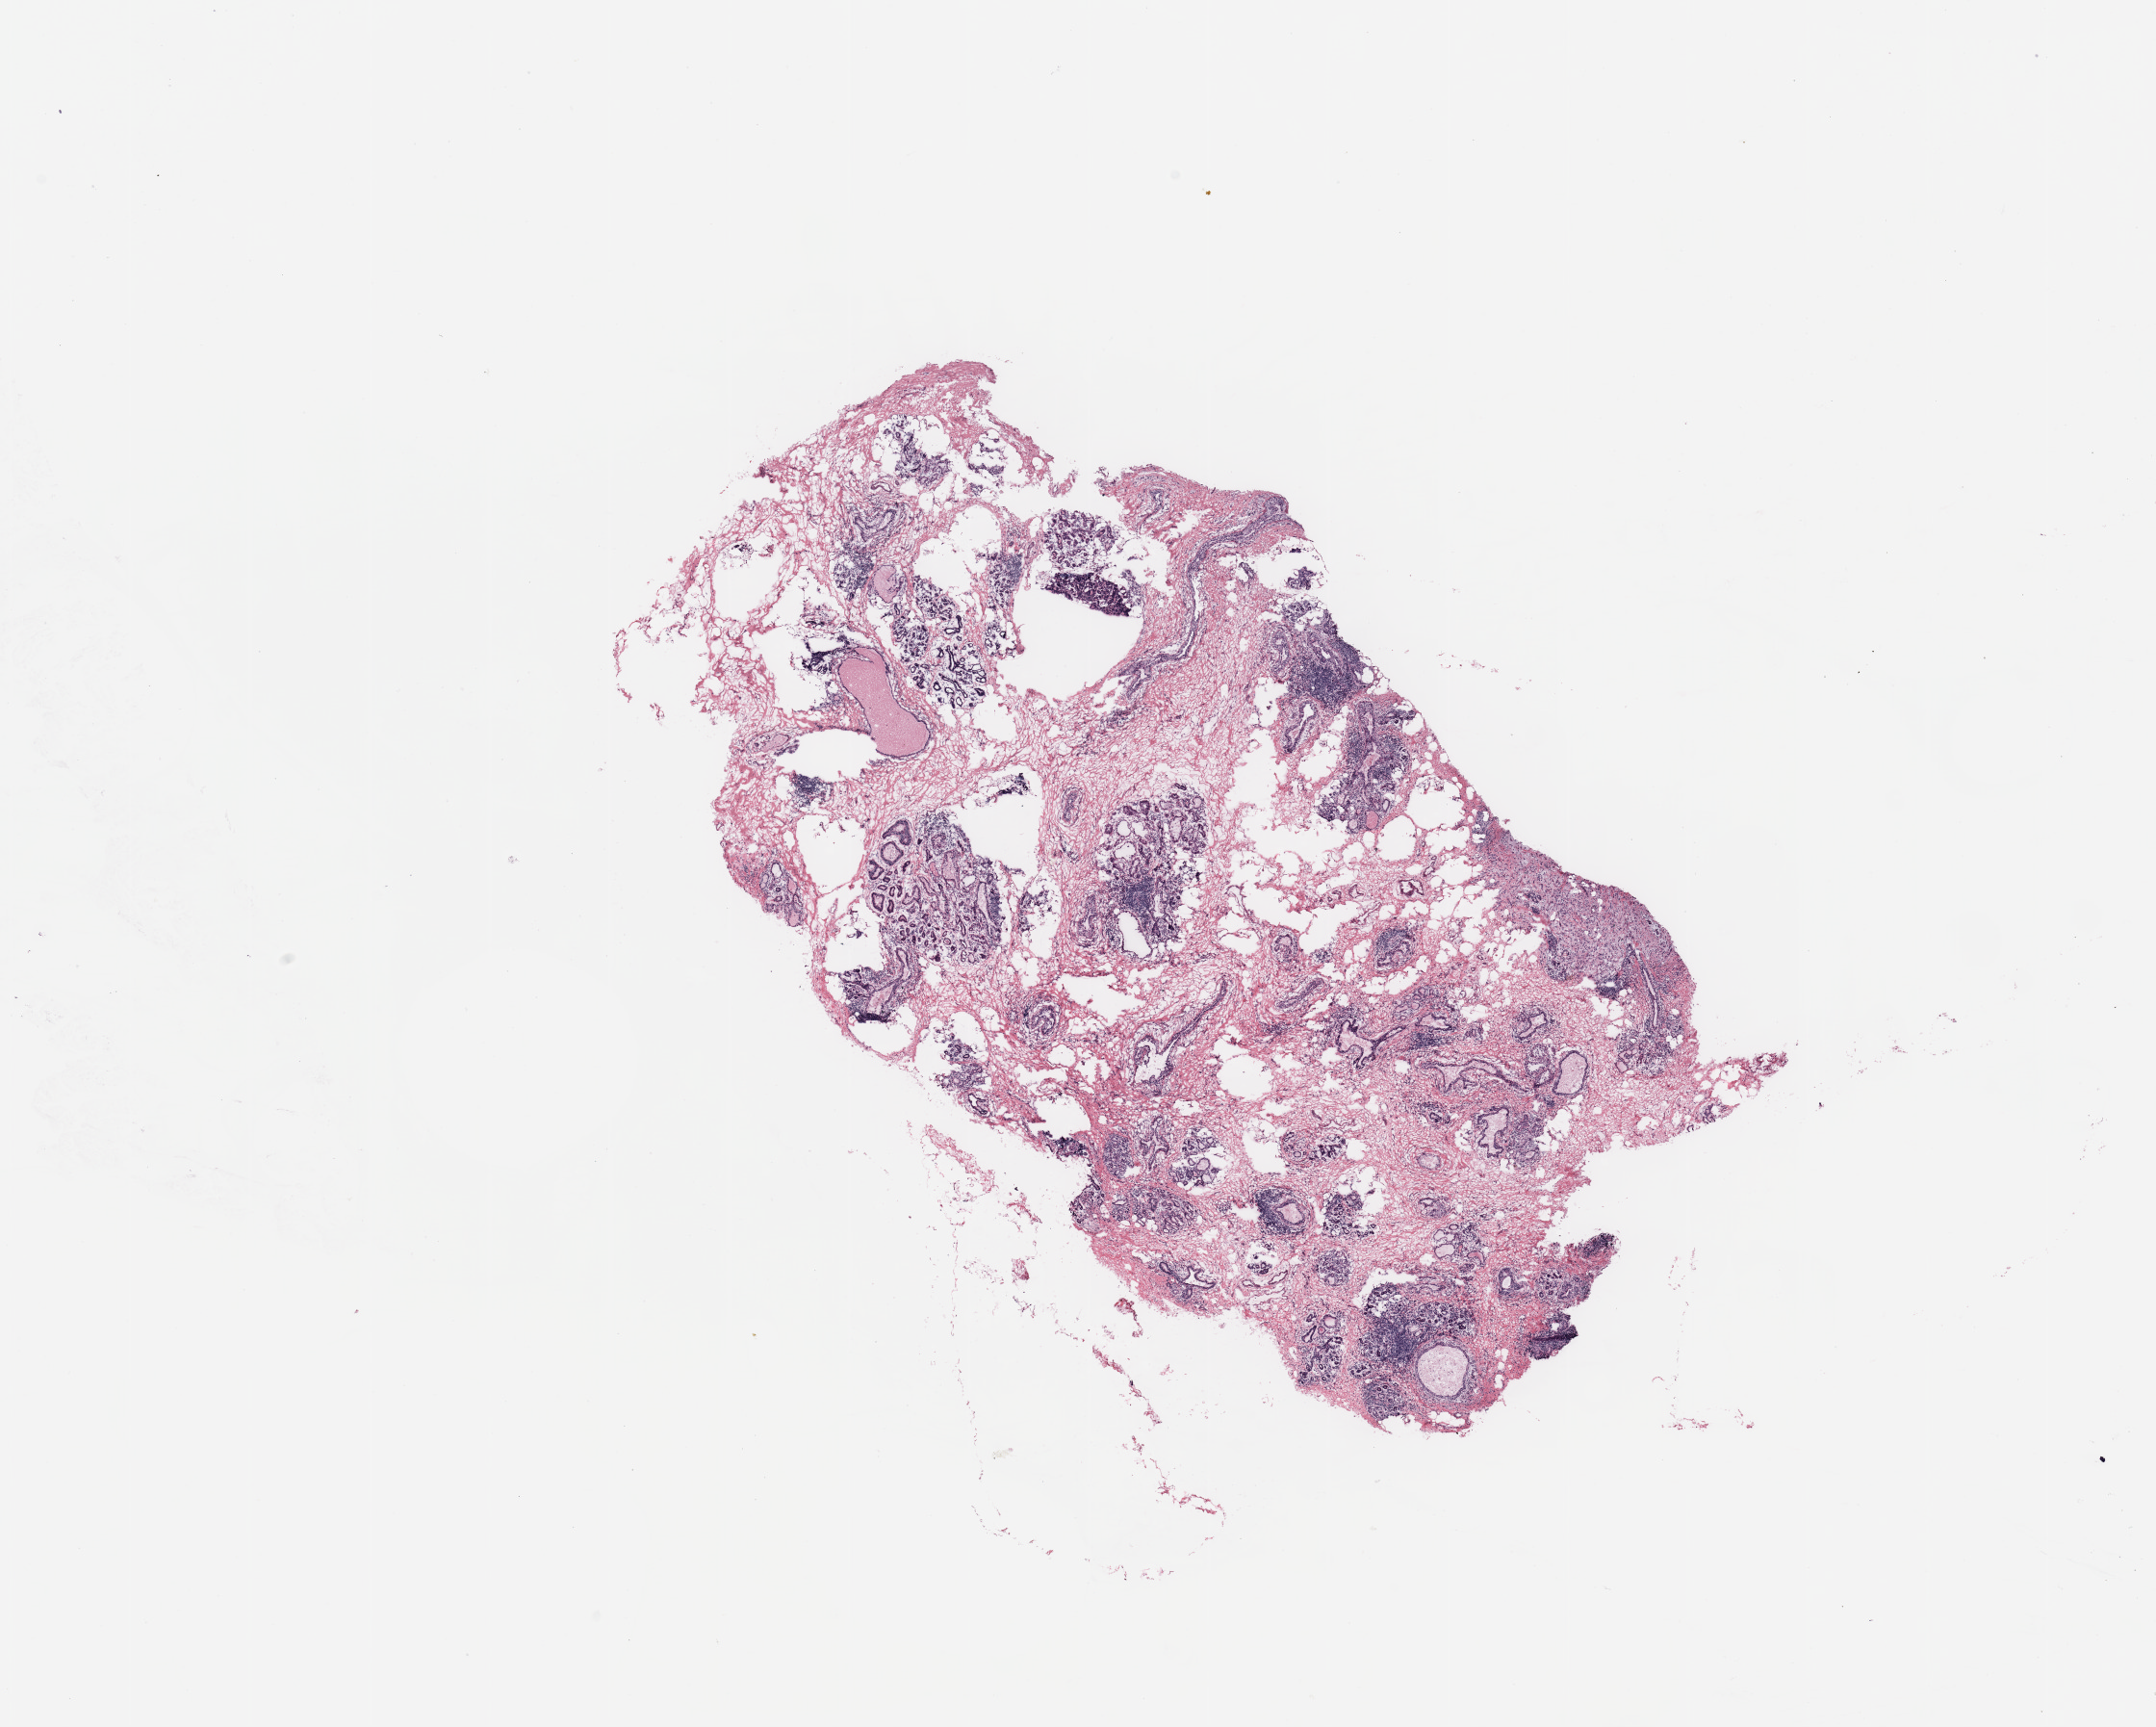
Digitized Hematoxylin and eosin (H&E) stained tissue section (whole slide) — whole scanned area (about 17.7 x 14.2 mm, from a 20x scan) shown as a low-resolution overview. Breast, tissue type not recorded.
Patient diagnosis (cohort enrolment): breast cancer (breast).